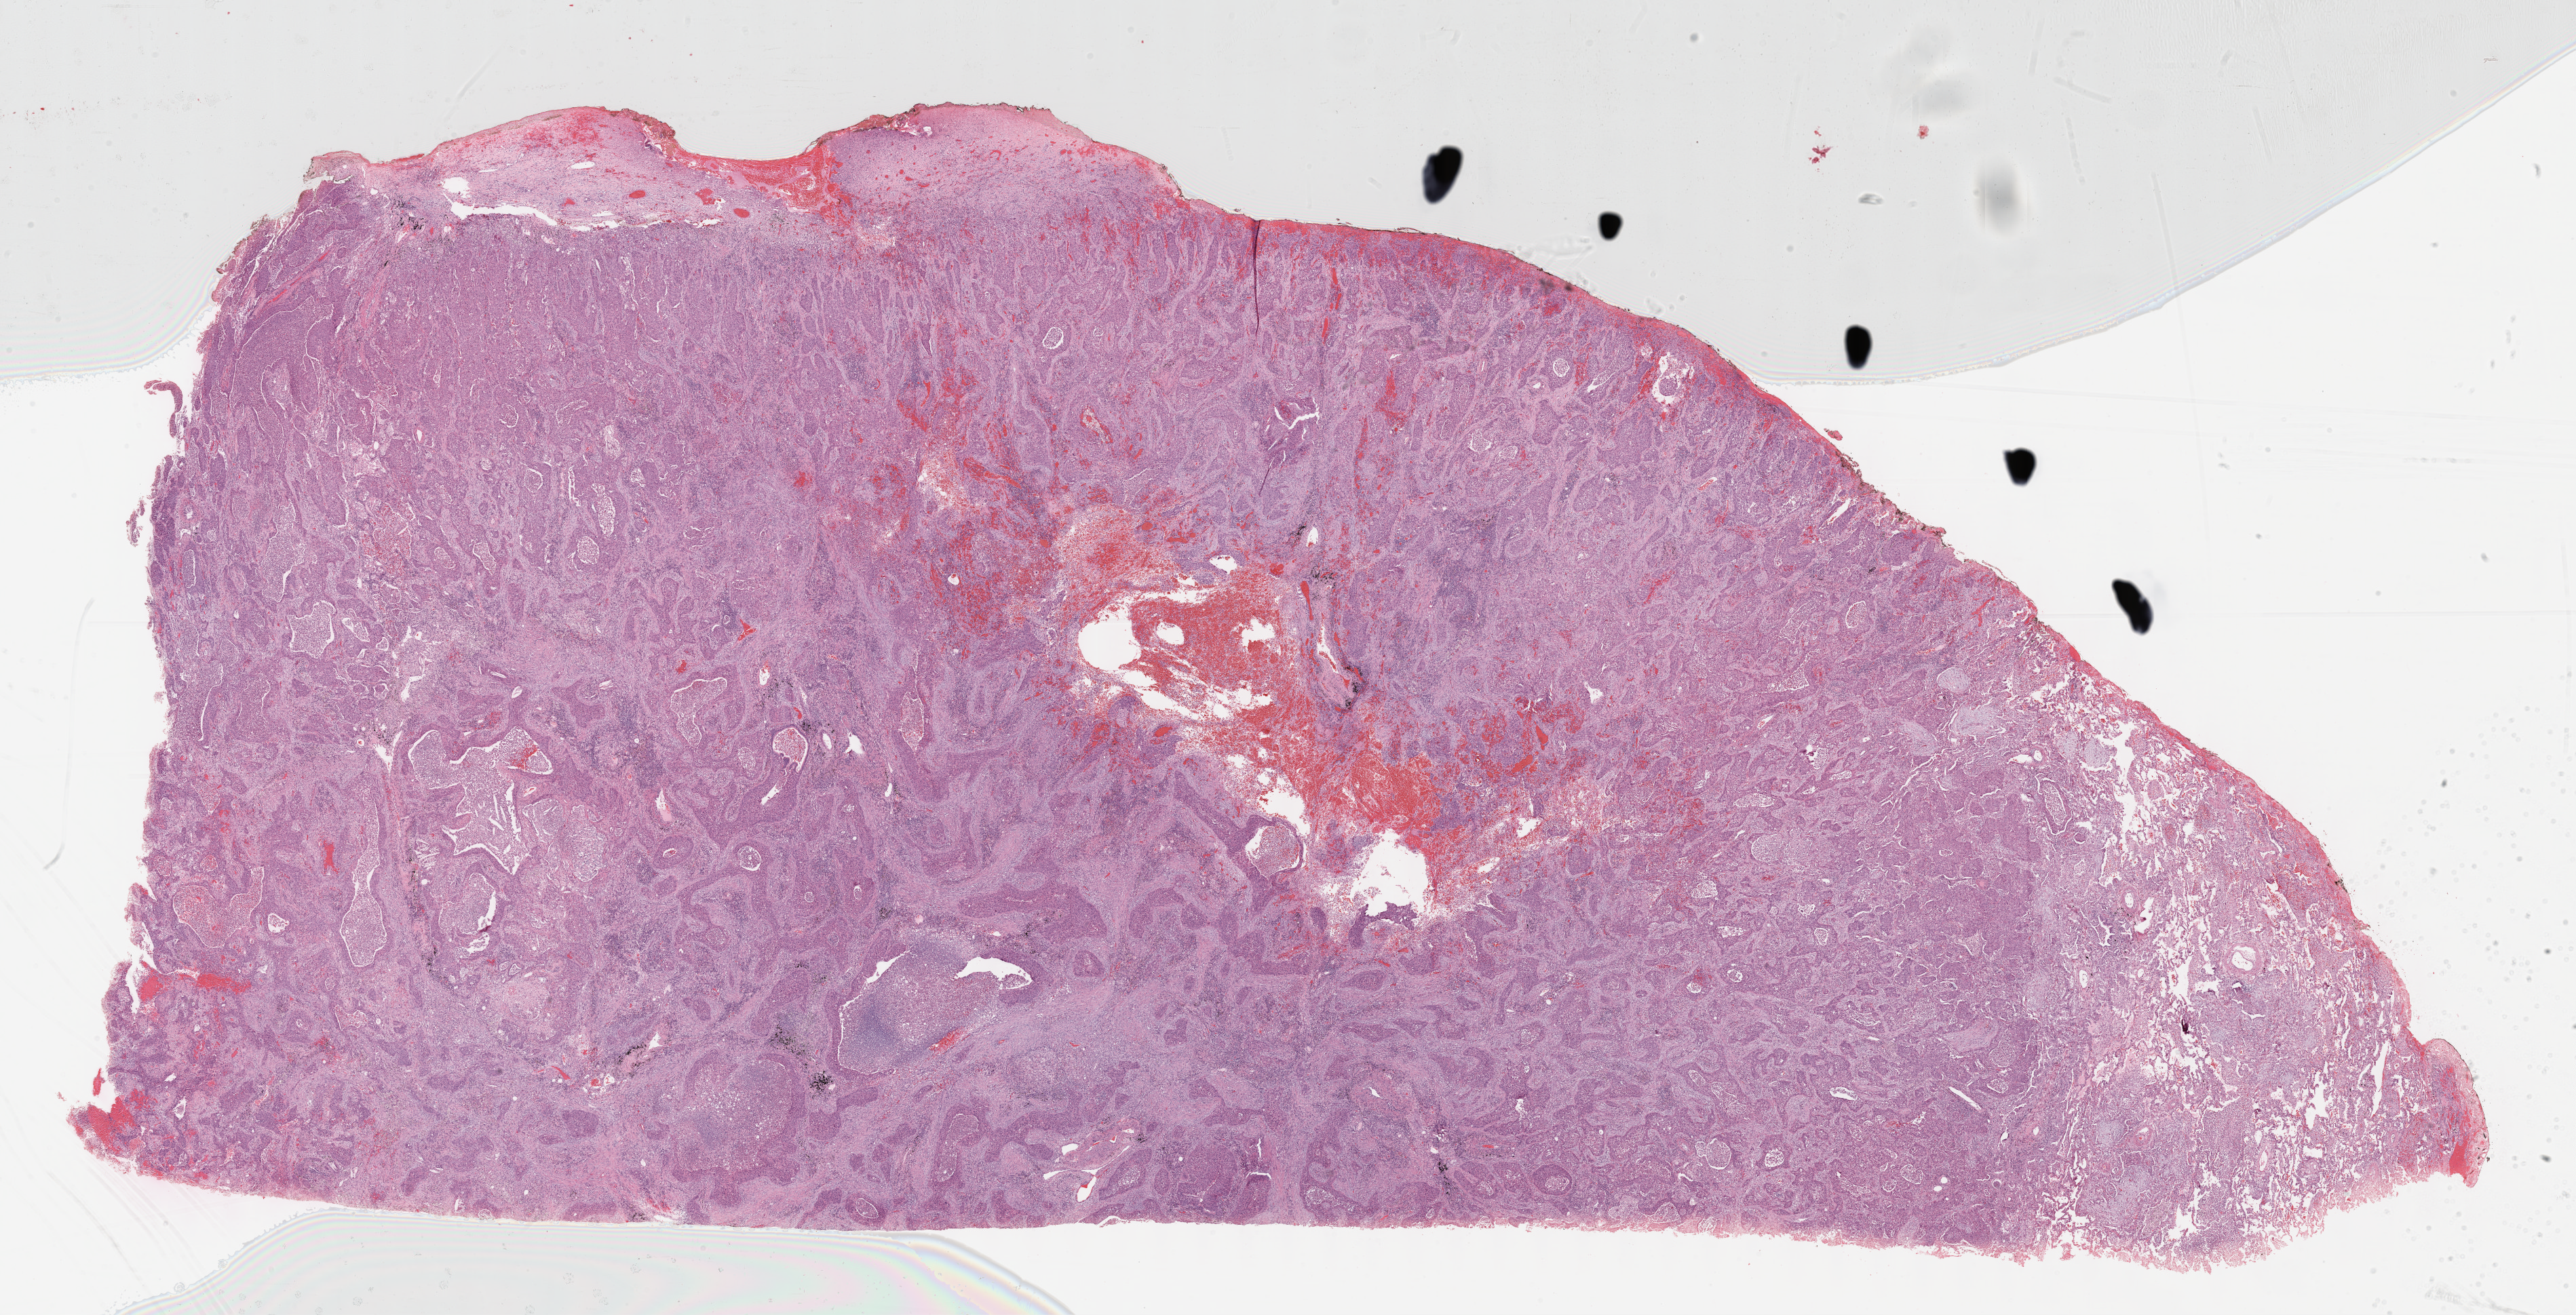
Whole-slide histology image, H&E-stained — whole scanned area (about 30.7 x 15.7 mm, slide scanned at 40x) shown as a low-resolution overview, formalin-fixed paraffin-embedded (FFPE) diagnostic section, lung, primary tumour sample. Female, age 81 years at initial diagnosis.
Laterality: left. AJCC pathologic stage: IB. Pathologic diagnosis: Squamous cell carcinoma, NOS (lower lobe, lung).